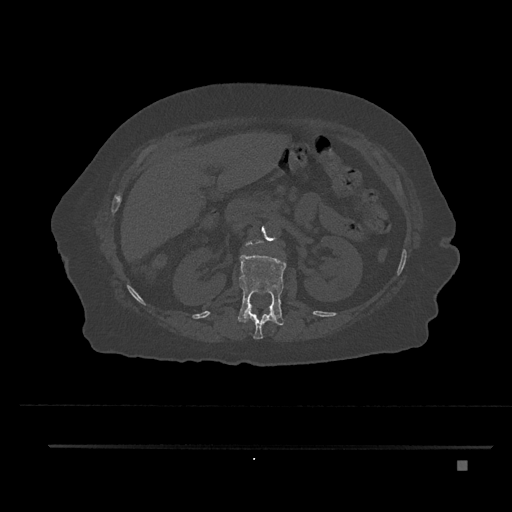
CT including the spine, one axial slice. Slice 230 of 797 in the series (ordered by position). 120 kVp. Bone window (W 1800 / L 400 HU). 0.5 mm slice thickness. 512 × 512 image matrix, field of view 437 × 437 mm. Patient: female, 76 years. From the clinical record (not read from this slice): primary cancer: lung.
Outlined on this slice (semi-automatic segmentation, software-assisted and operator-edited):
- L1 vertebra: bounding box <238,253,286,326> (left, top, right, bottom; pixels)
- L2 vertebra: <246,239,259,247>
- T12 vertebra: <244,306,277,339>